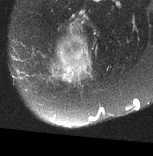
MRI of an extremity soft-tissue mass, one axial slice. Position 21 of 77 along the scan axis. T2-weighted fat-saturated. MR volume resampled by the dataset authors to the PET/CT grid (not the native acquisition matrix). 3.27 mm slice thickness. 153 × 156 image matrix, field of view 149 × 152 mm. Female patient. From the clinical record (not read from this slice): histological type: synovial sarcoma; grade: intermediate; site of the primary tumour: right buttock.
Outlined on this slice (expert contour drawn on MRI and transferred to this co-registered scan by the dataset authors):
- gross tumour volume including surrounding oedema: bounding box <49,22,91,85> (left, top, right, bottom; pixels)
- gross tumour volume (mass): <49,34,91,83>